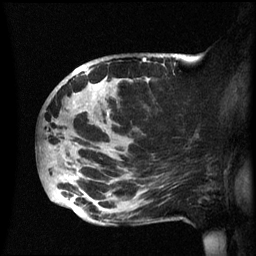
Breast MRI (dynamic contrast-enhanced), one sagittal slice. Slice 30 of 60 in the series (ordered by position). Dynamic contrast-enhanced series, image 2 of 3 at this slice position (ordered by acquisition). 1.5 T. TE 4.2 ms, TR 8.4 ms. 2.4 mm slice thickness. 256 × 256 image matrix. Female patient, age 49 years.
Outlined on this slice (semi-automatic segmentation, software-assisted and operator-edited):
- analysis volume of interest (the breast-tissue region the enhancement analysis was run in; not a lesion): bounding box [x1, y1, x2, y2] px = [39, 54, 174, 226]
- tumour enhancement mask (voxels above the 70 % enhancement threshold inside the analysis volume of interest): [86, 60, 150, 116]